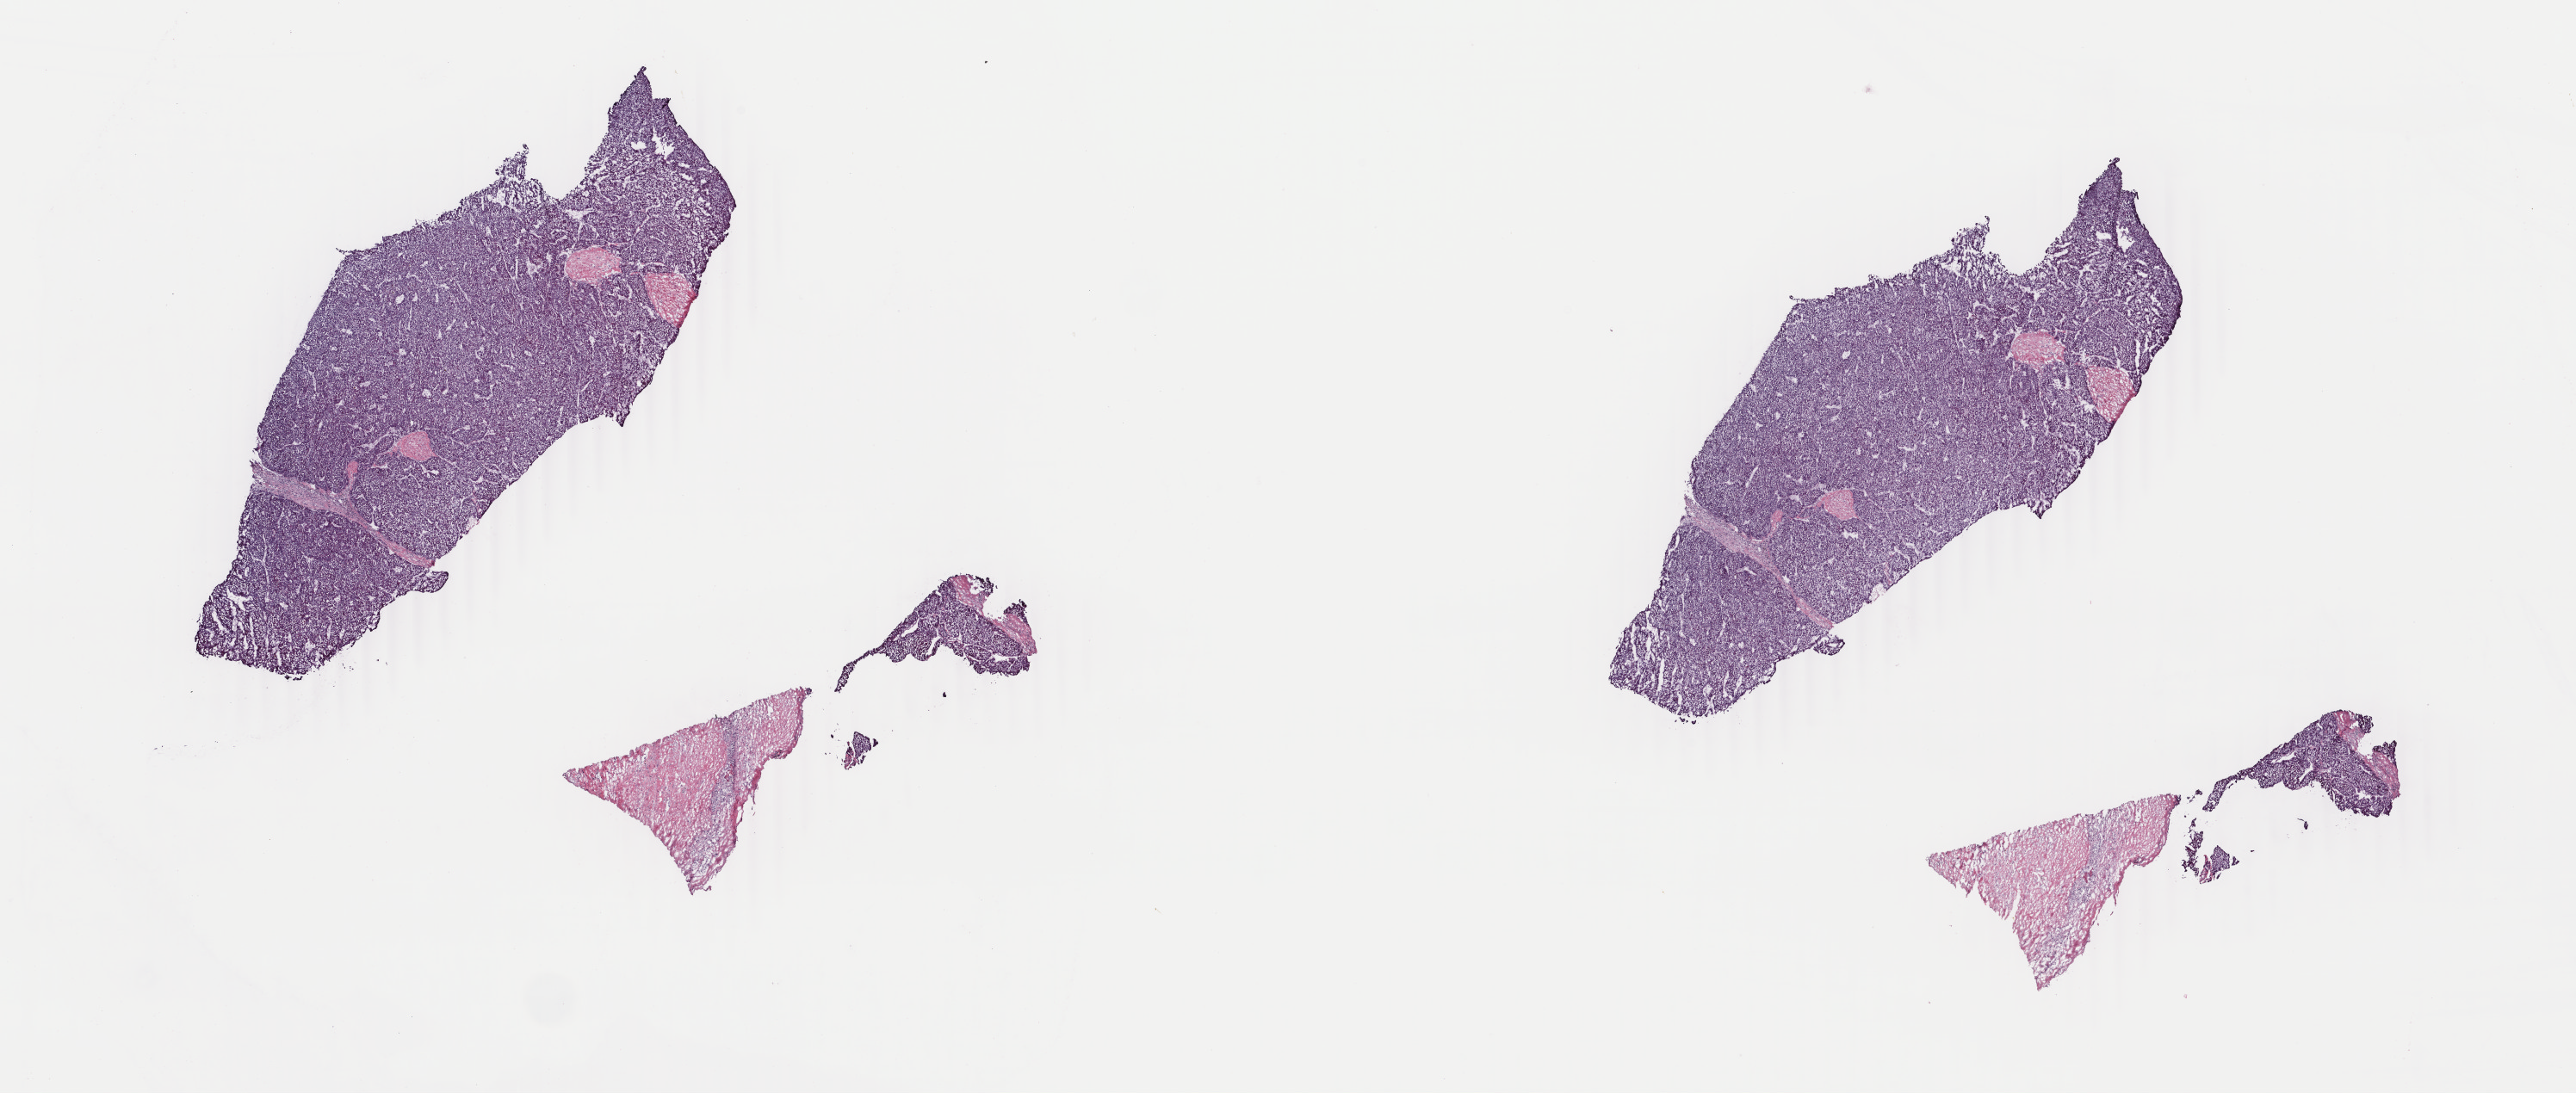
Digitized H&E-stained tissue section (whole slide) — a low-resolution overview of the entire scanned area, about 23.8 x 10.1 mm, frozen section, primary tumour sample from the liver. Male, age 69 years at initial diagnosis. Composition of this section per pathologist review: tumour cells 90%, tumour nuclei 80%.
Diagnosis: Hepatocellular carcinoma, NOS.